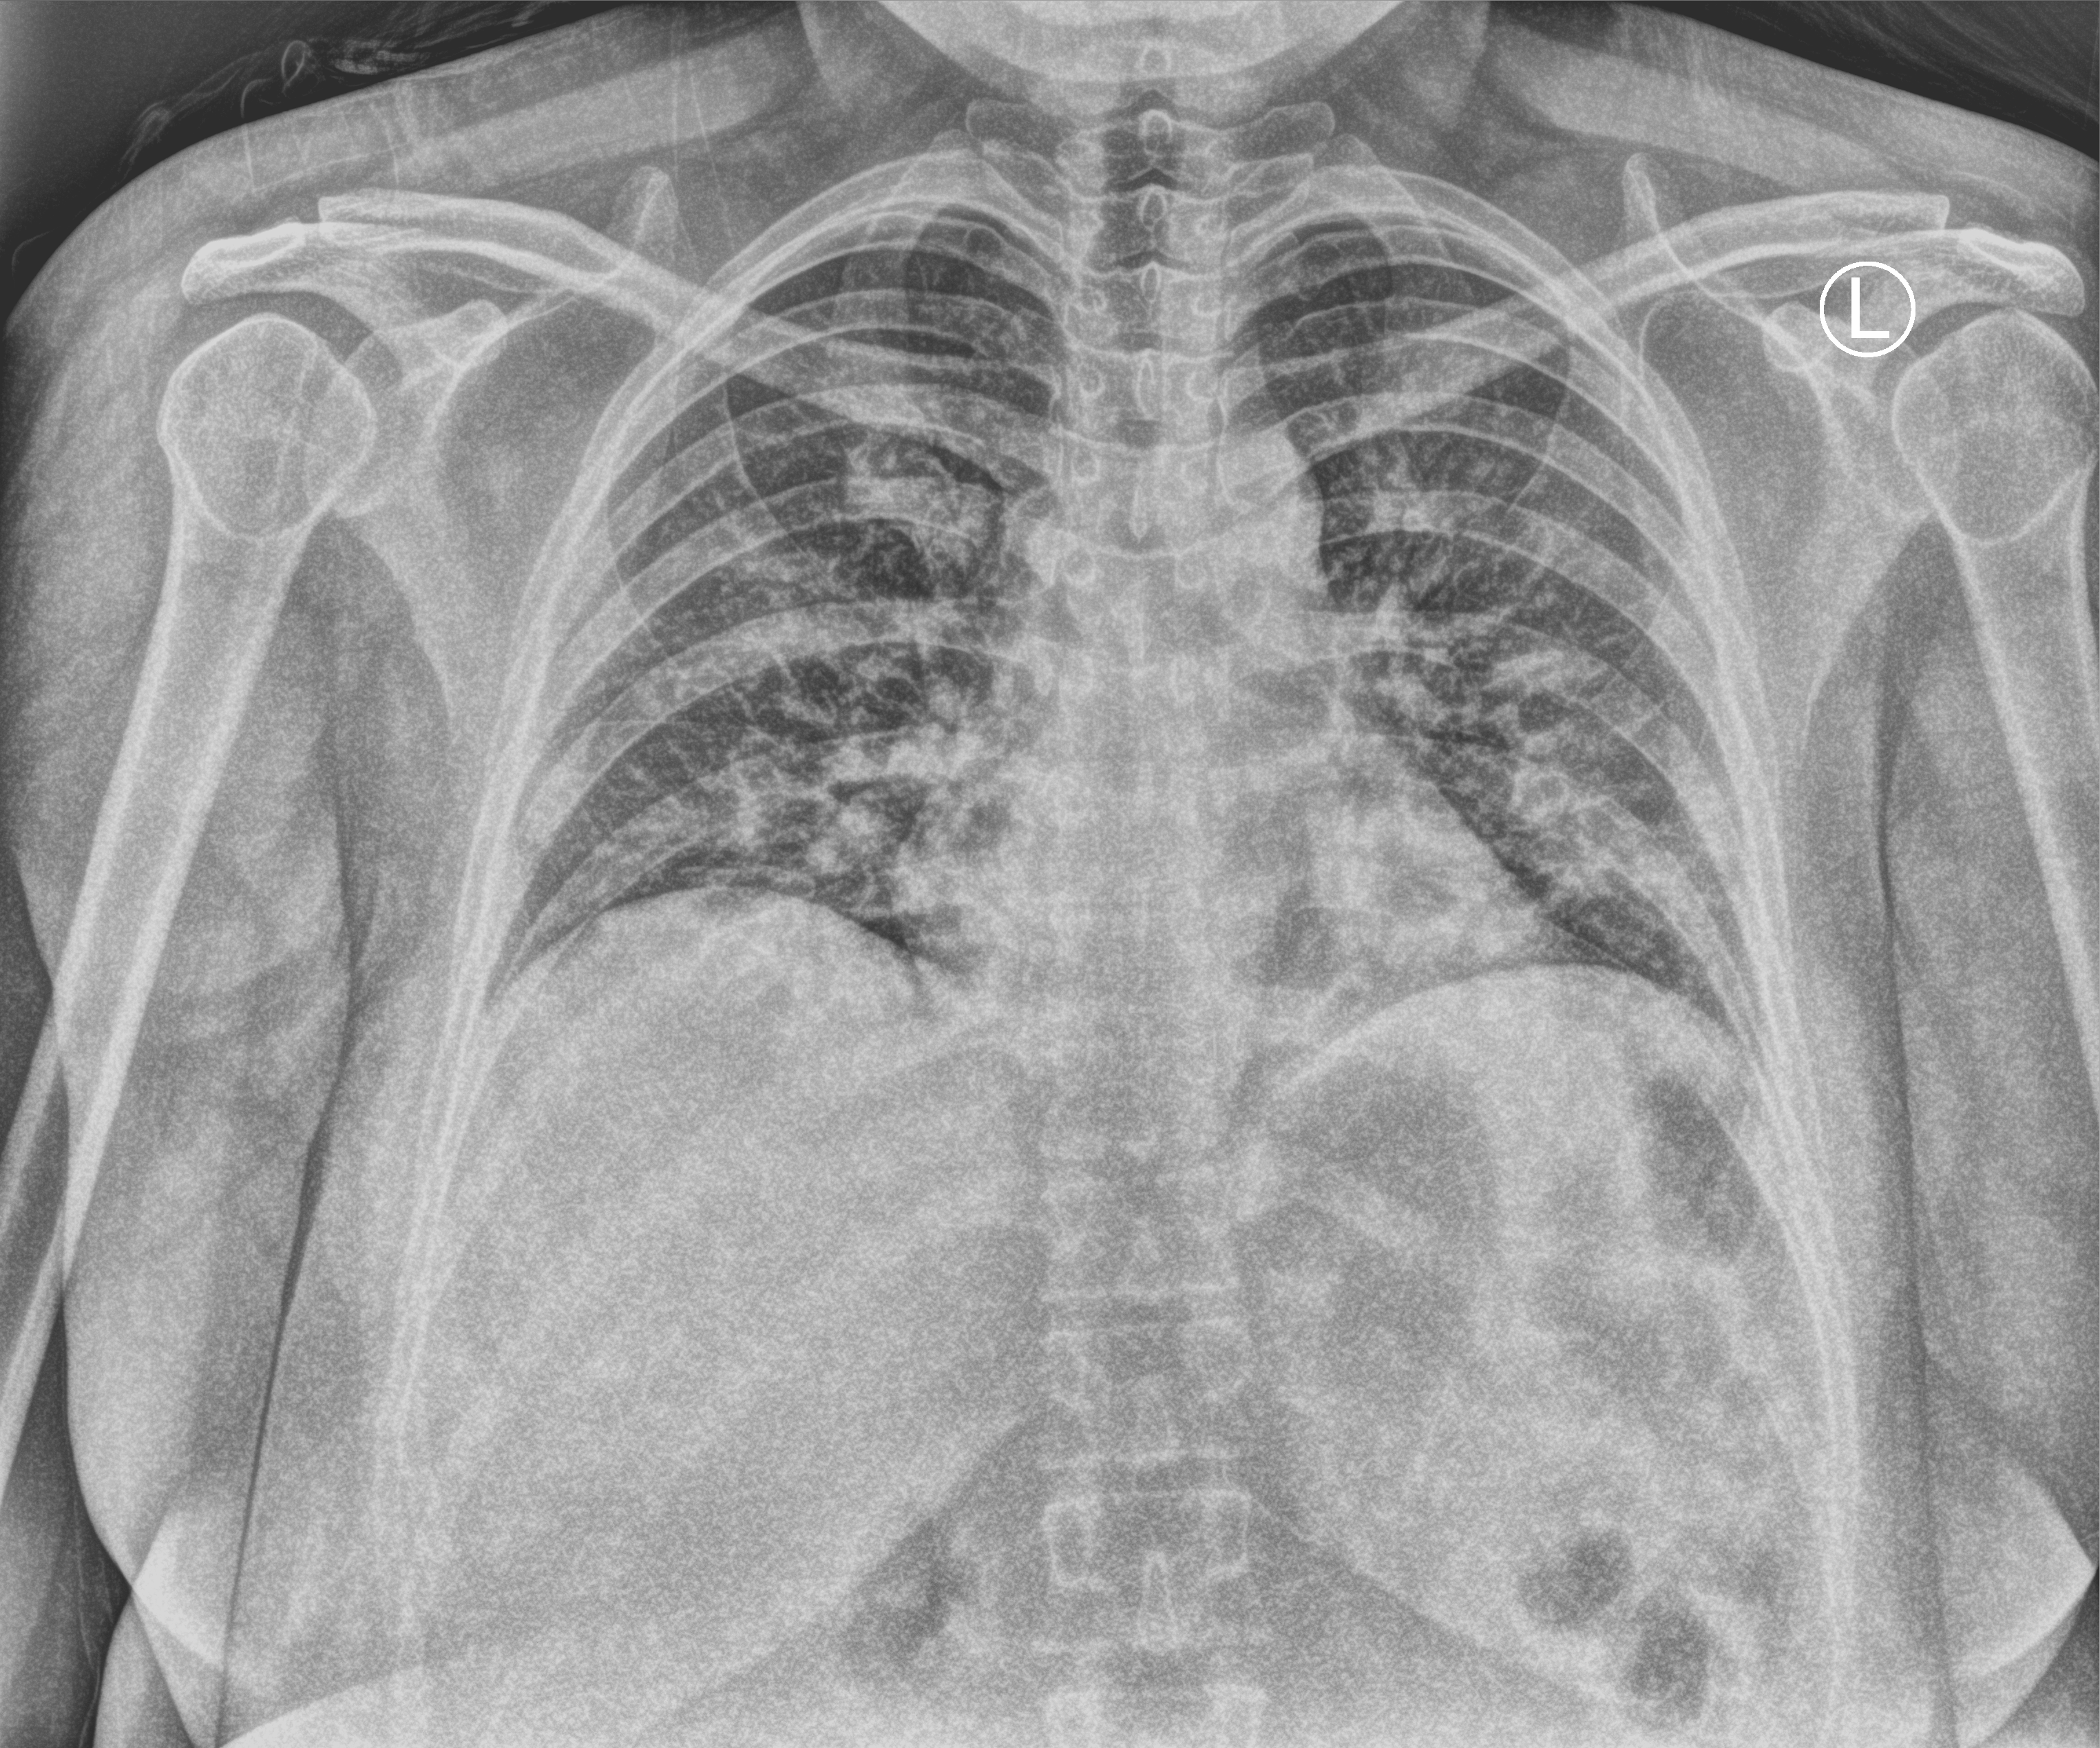
Portable chest radiograph, anteroposterior (AP) projection. Female patient hospitalised with COVID-19, age 18–59 years.
From the hospital-stay record, not from the radiograph (when in the stay this image was taken is not recorded):
- mechanically ventilated during this hospital stay: no
- admitted to intensive care during this hospital stay: no